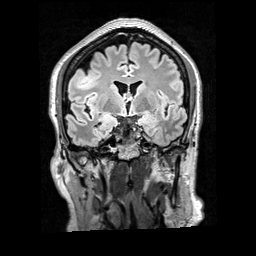
Brain MRI from a brain-tumour surgery series, one coronal slice. Position 110 of 200 along the scan axis. T2 FLAIR. 1 mm slice thickness. 256 × 256 image matrix, field of view 256 × 256 mm. Case-level facts recorded for this patient, not image findings: histopathology: Glioblastoma; WHO grade: 4; IDH mutation: no.
Structures marked on this image (outlined manually by an expert reader):
- tumour: bounding box (x1, y1, x2, y2) in pixels: (74, 71, 101, 90)